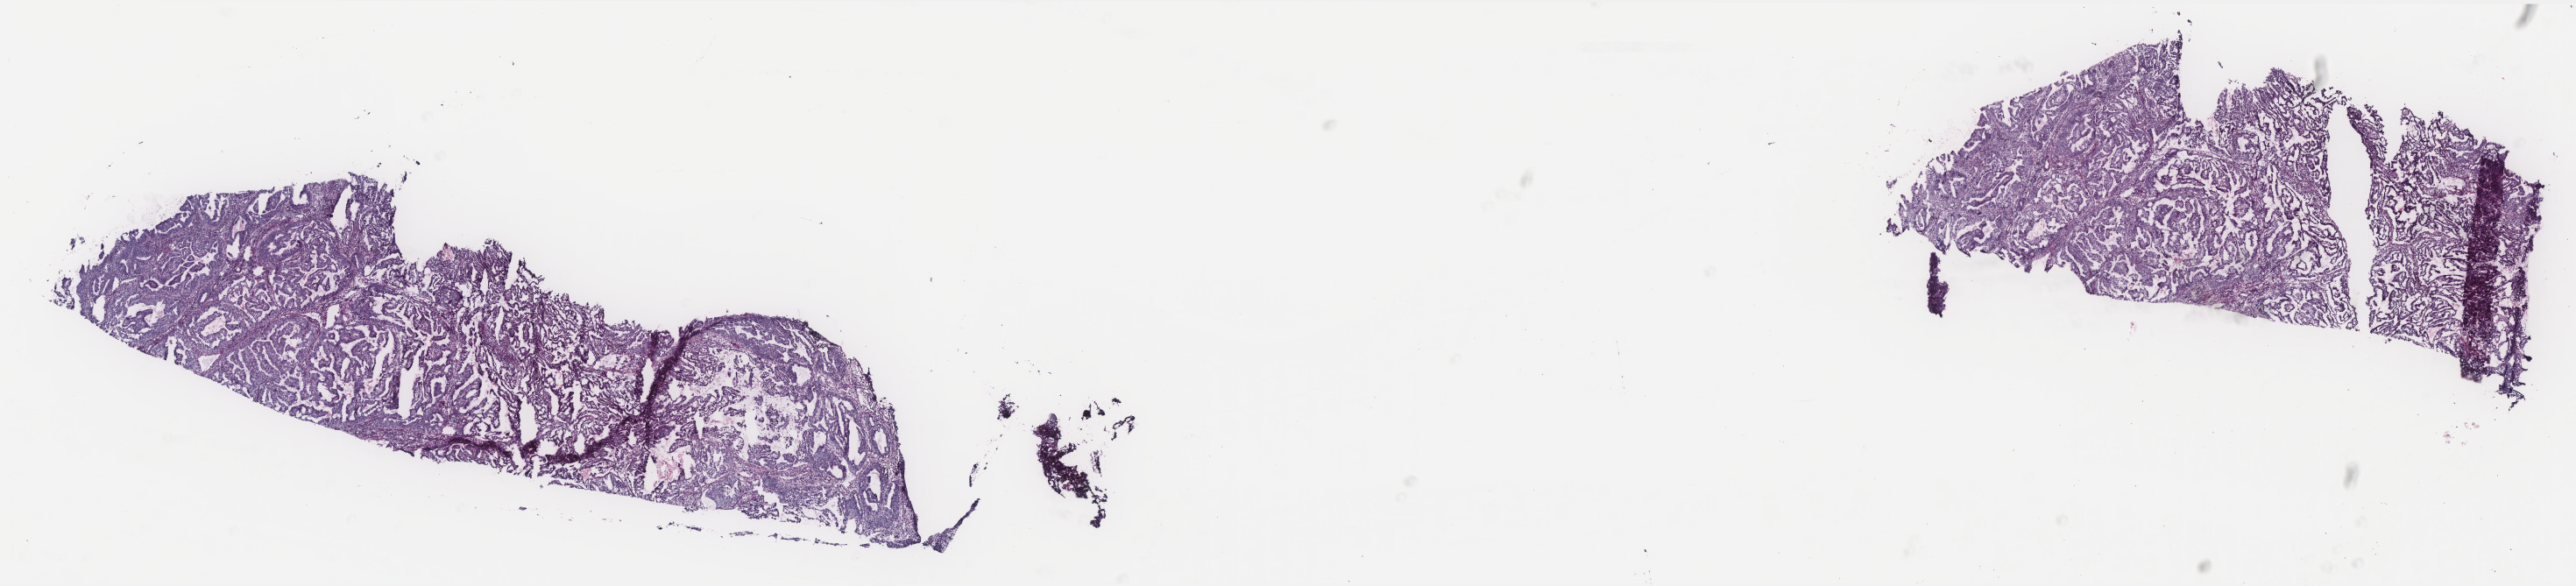
Whole-slide histology image, H&E — whole scanned area (about 23.6 x 5.4 mm, slide scanned at 40x) shown as a low-resolution overview. Frozen section from the top of the tissue portion. Sample: primary tumour, uterus. Female patient; age at initial diagnosis 37 years. Histologic grade: G1 (well differentiated). Pathologist review of this section (percent, as recorded): tumour cells 80%, tumour nuclei 90%, normal cells 0%, stromal cells 10%, necrosis 10%. Infiltration values recorded for this section: lymphocyte infiltration 20%, monocyte infiltration 0%, neutrophil infiltration 10%.
- FIGO stage: IA
- histologic diagnosis: Endometrioid adenocarcinoma, NOS (endometrium)